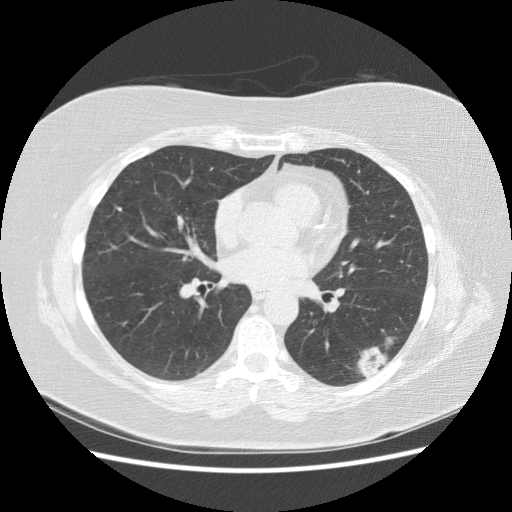
Low-dose screening chest CT, axial slice; third screening round (two years after baseline); lung window (W 1500 / L -600 HU); 2.5 mm slice thickness; 512 × 512 image matrix, field of view 360 × 360 mm. Female participant, aged 57 years at enrolment. Current smoker at enrolment.
Expert reader's lesion annotation, bounding box <336,324,406,388> (left, top, right, bottom; pixels). Reader record for this screening exam (exam-level; its link to the box is not recorded): non-calcified nodule or mass ≥4 mm, left lower lobe, 40 × 20 mm, poorly defined margins, mixed attenuation, pre-existing on the prior screen: yes; interval growth: yes. Official screen result: positive, other. Lung cancer was diagnosed 55 days after this screen: squamous cell carcinoma, NOS, left lower lobe, poorly differentiated (G3), stage IB (AJCC 6th edition), 40 mm at pathology.